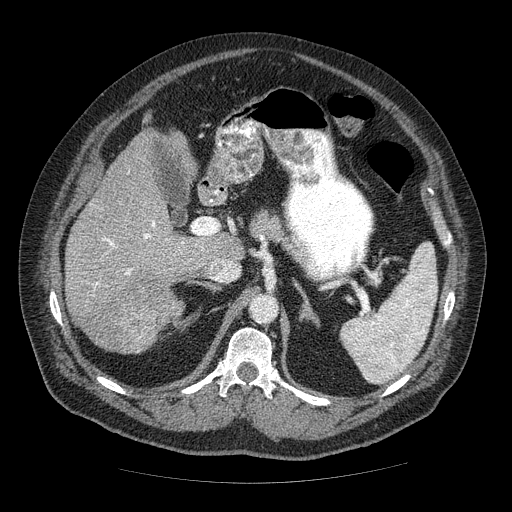
Contrast-enhanced abdominal CT (liver protocol), one axial slice. Position 32 of 85 along the scan axis. Reconstruction kernel STANDARD. Soft-tissue window (W 400 / L 40 HU). 2.5 mm slice thickness. 512 × 512 image matrix, field of view 420 × 420 mm. From the clinical record (not read from this slice): diagnosis: hepatocellular carcinoma (patient treated with transarterial chemoembolisation; whether this scan precedes or follows treatment is not stated here); TNM stage (as recorded): Stage-IIIA; Child-Pugh class: A; tumour nodularity: multinodular; tumour size: 7 cm.
Outlined on this slice (semi-automatically segmented with operator editing):
- liver parenchyma outside the tumour (the mass and vessels are separate outlines, so this box may not span the whole liver): bounding box (x1, y1, x2, y2) in pixels: (64, 130, 244, 333)
- mass: (80, 276, 183, 354)
- liver vessels: (92, 220, 235, 296)